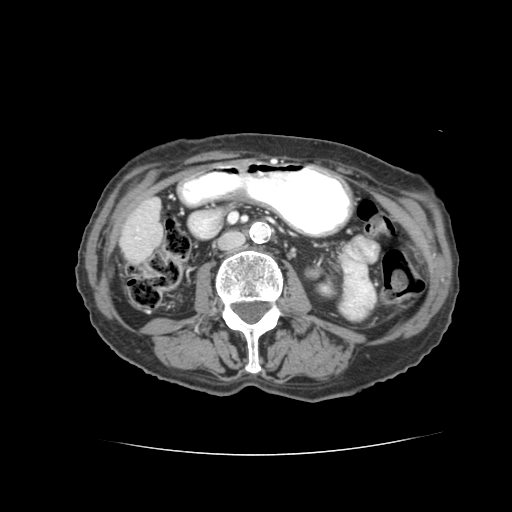
Contrast-enhanced abdominal CT (liver protocol), one axial slice; slice 10 of 77 in the series (ordered by position); reconstruction kernel STANDARD; 120 kVp; soft-tissue window (W 400 / L 40 HU); 512 × 512 image matrix. From the clinical record (not read from this slice): diagnosis: hepatocellular carcinoma (patient treated with transarterial chemoembolisation; whether this scan precedes or follows treatment is not stated here); TNM stage (as recorded): Stage-I; Child-Pugh class: A; tumour nodularity: uninodular.
Structures marked on this image (semi-automatically segmented with operator editing):
- liver parenchyma outside the tumour (the mass and vessels are separate outlines, so this box may not span the whole liver): bounding box <122,196,156,247> (left, top, right, bottom; pixels)